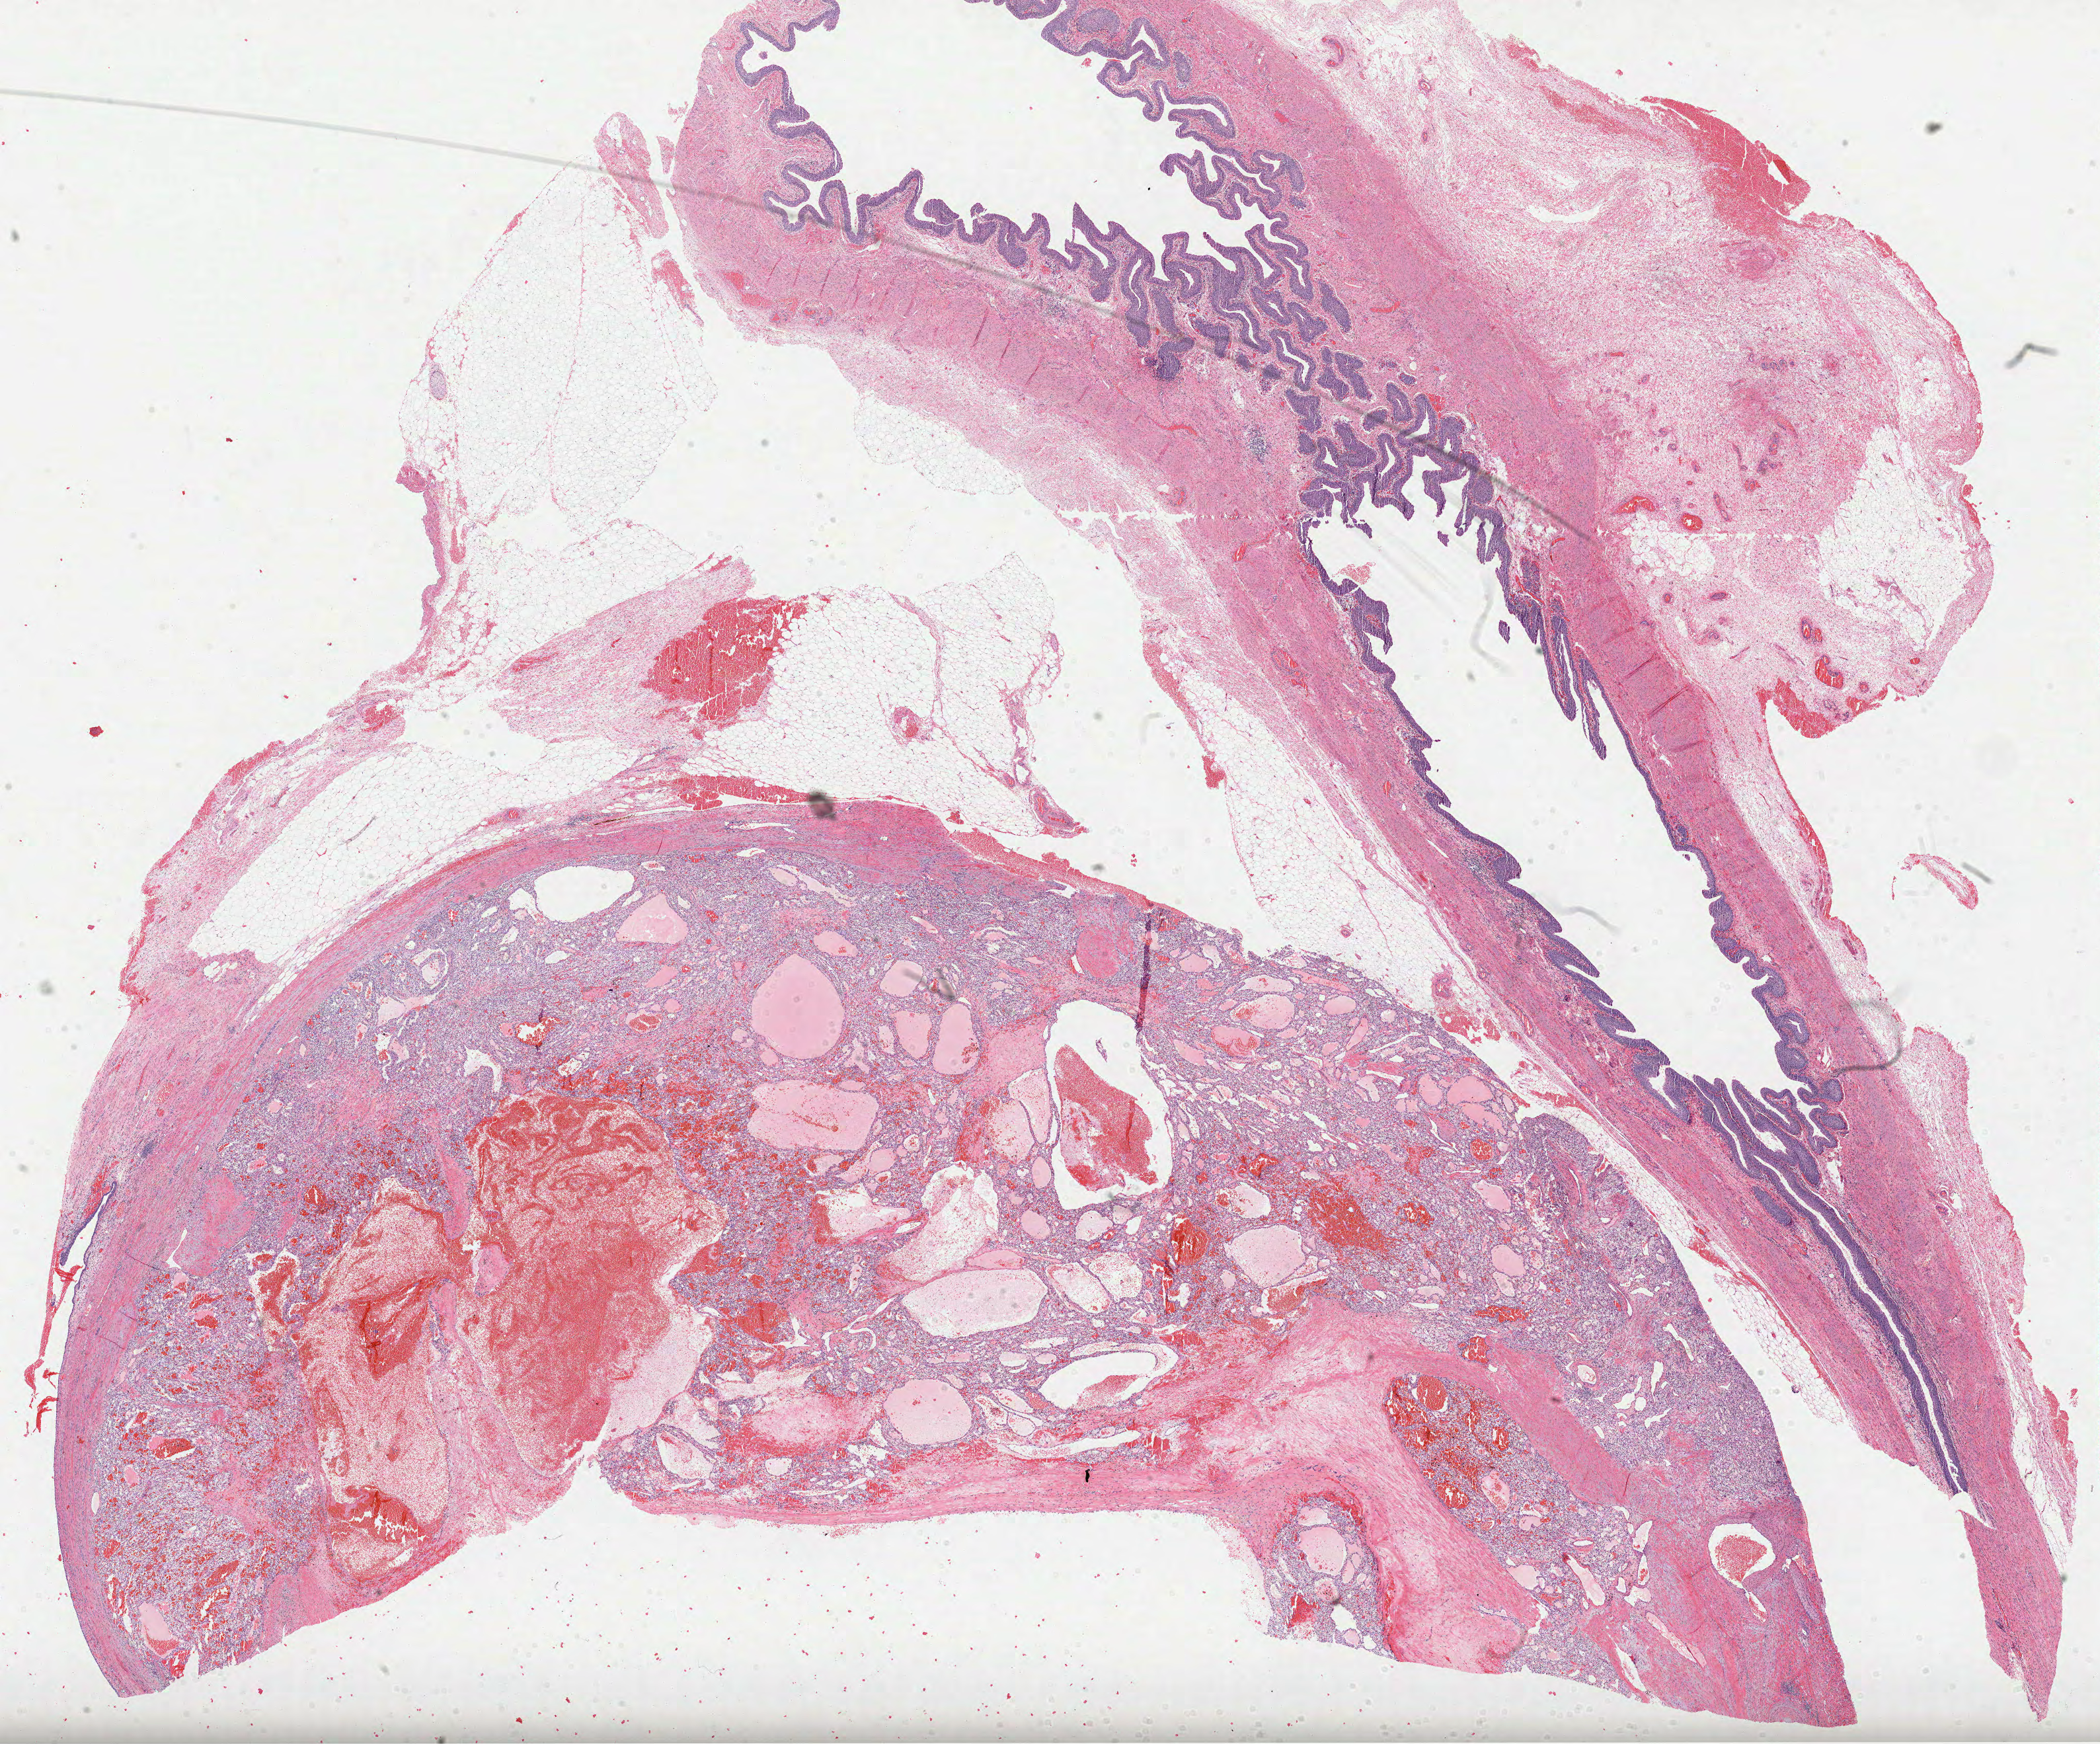
Hematoxylin and eosin (H&E) stained whole-slide image, shown as a low-resolution overview of the whole scanned area (about 25.6 x 21.3 mm); formalin-fixed paraffin-embedded (FFPE) diagnostic section; primary tumour sample from the kidney. Patient: female, age at initial diagnosis 67 years. Histologic grade: G3 (poorly differentiated).
Diagnosis: Clear cell adenocarcinoma, NOS. AJCC pathologic stage: I (7th edition).